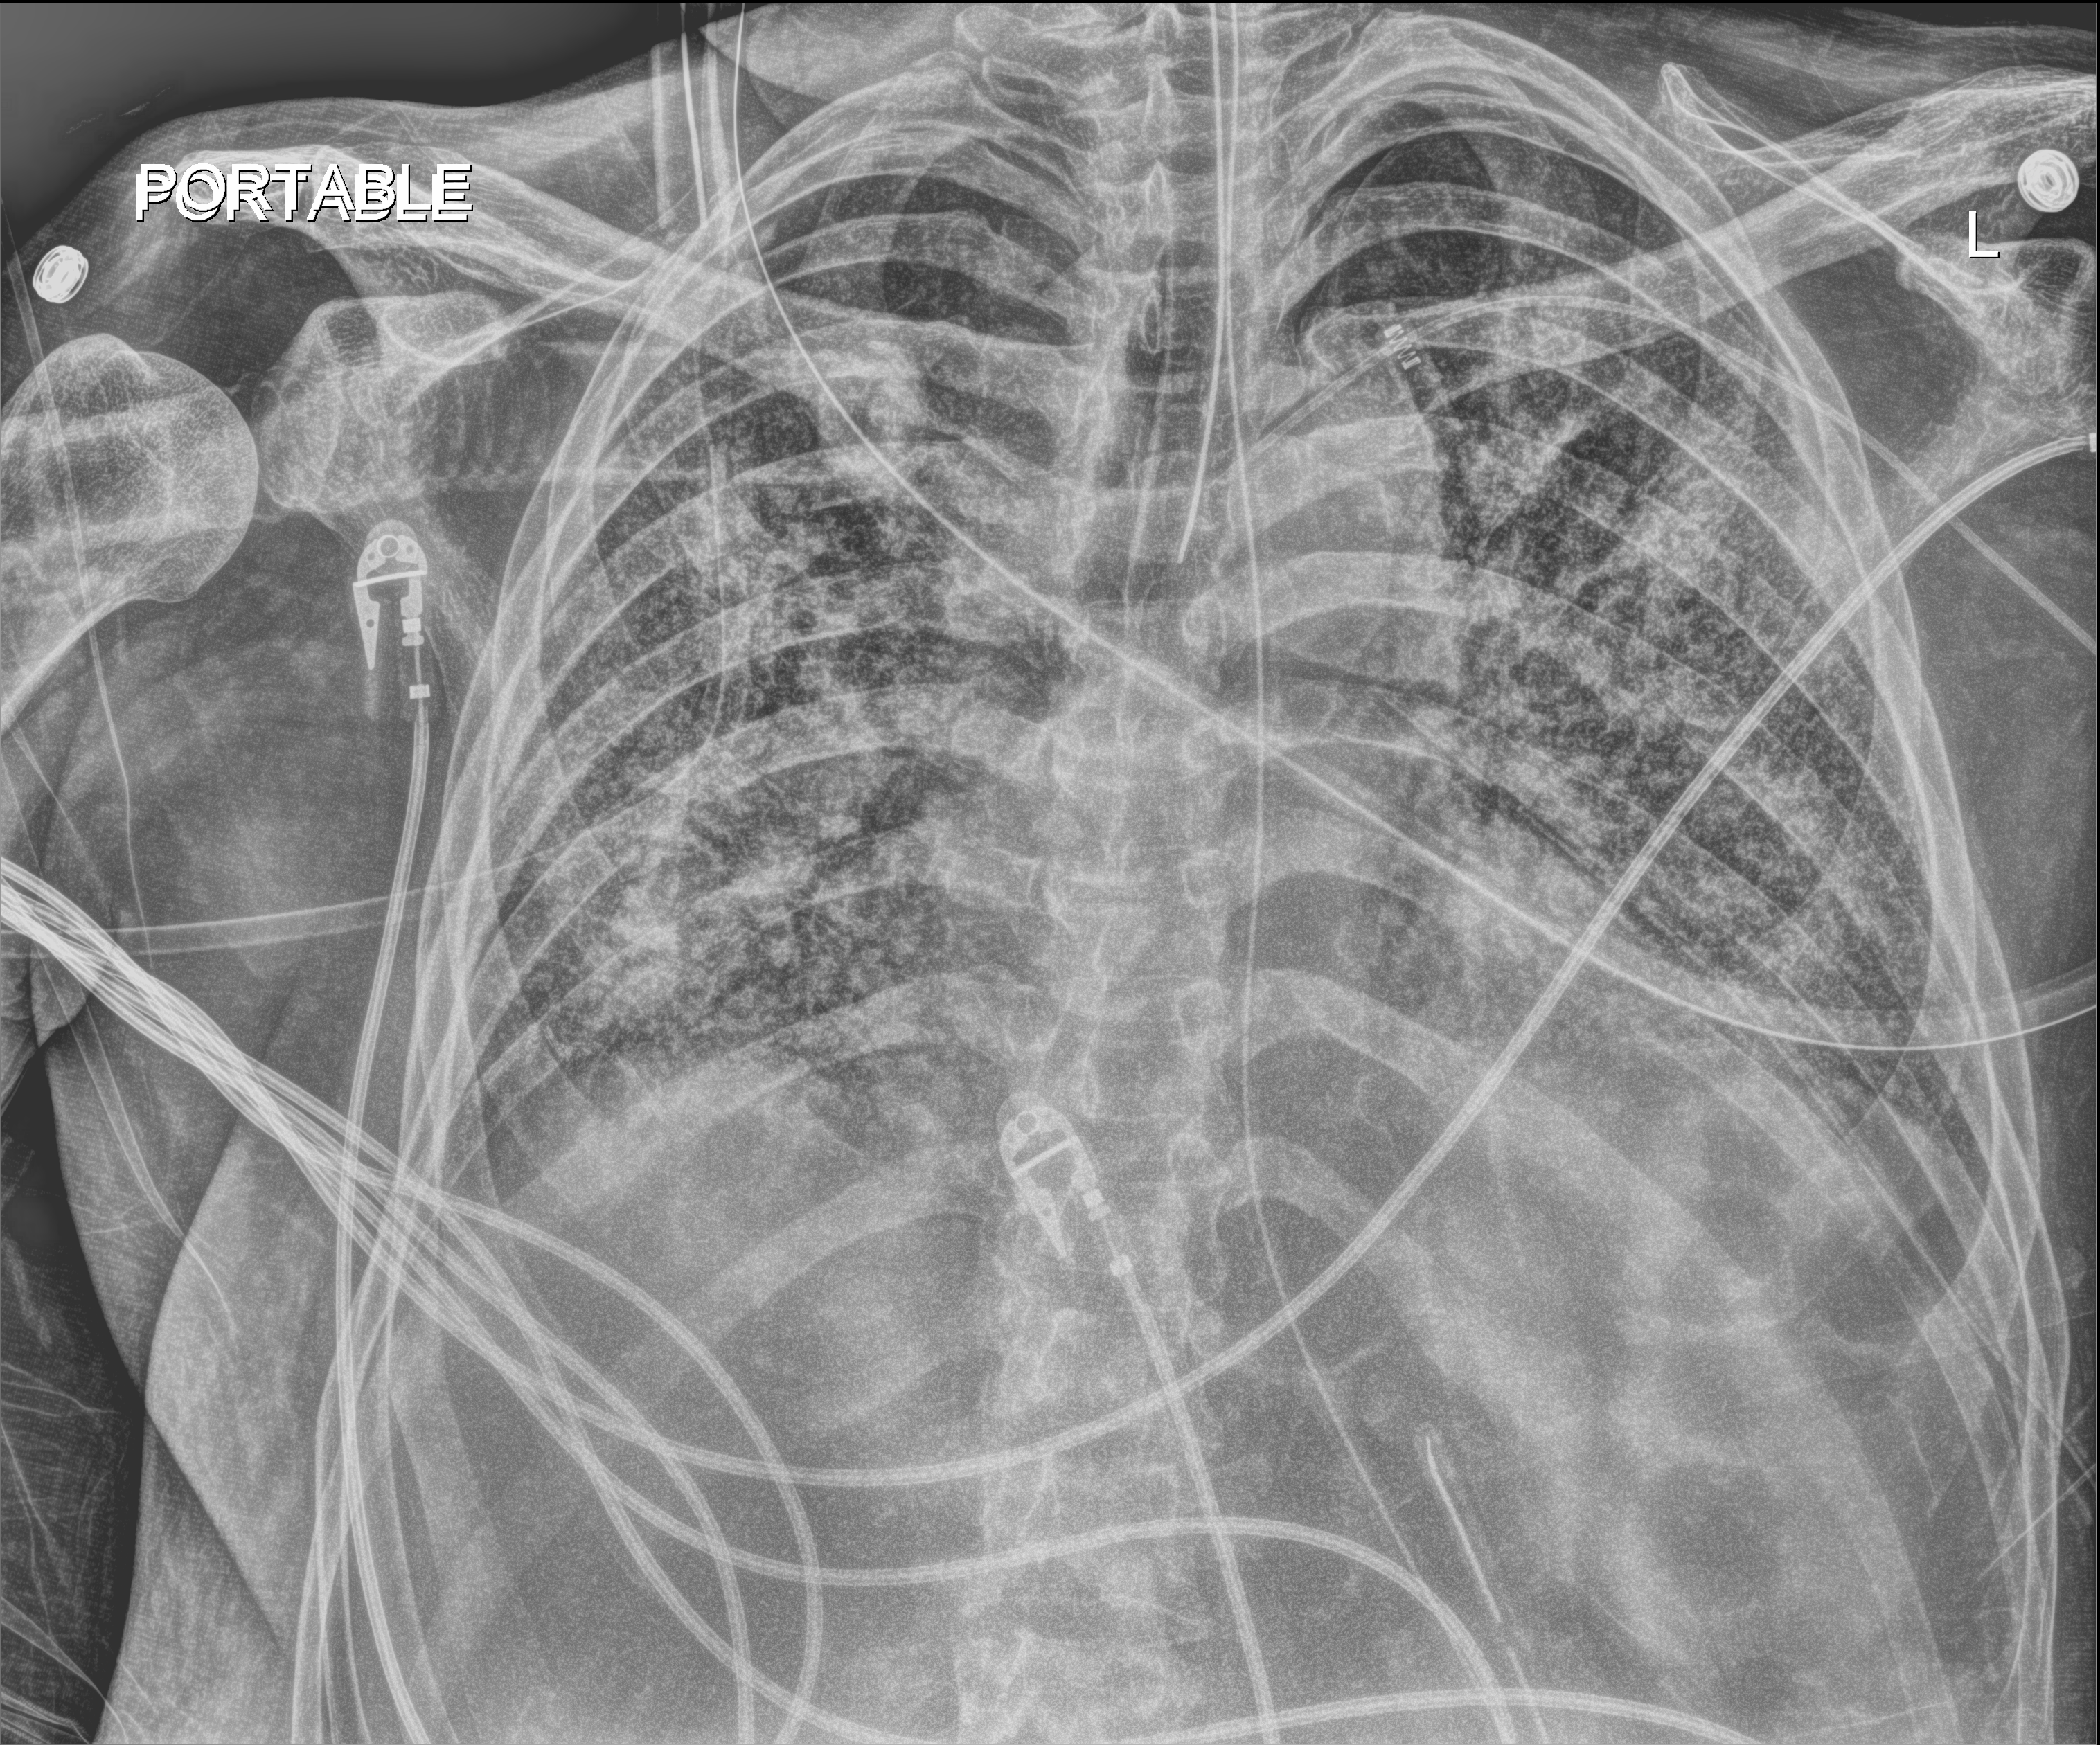
Chest X-ray (portable); anteroposterior (AP) projection. Male patient hospitalised with COVID-19, age 60–74 years.
From the hospital-stay record, not from the radiograph (when in the stay this image was taken is not recorded):
- admitted to intensive care during this hospital stay: yes